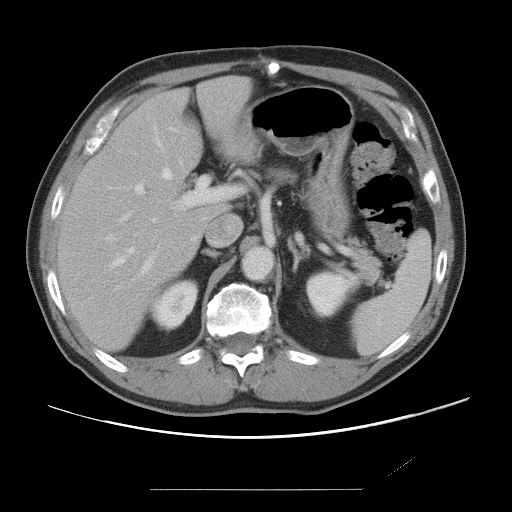
Contrast-enhanced abdominal CT, one axial slice; position 45 of 87 along the scan axis; 120 kVp; intravenous contrast given; soft-tissue window (W 400 / L 40 HU); 512 × 512 image matrix. Male patient, age 74 years. From the clinical record (not read from this slice): diagnosis: colorectal cancer liver metastases, imaged before liver resection; multiple liver metastases: yes.
Outlined on this slice (outlined manually by an expert reader):
- hepatic veins: bounding box (x1, y1, x2, y2) in pixels: (109, 142, 182, 265)
- liver: (60, 77, 254, 349)
- planned liver remnant (the part of the liver to remain after resection): (59, 77, 253, 349)
- portal vein (with intrahepatic branches): (120, 176, 241, 273)